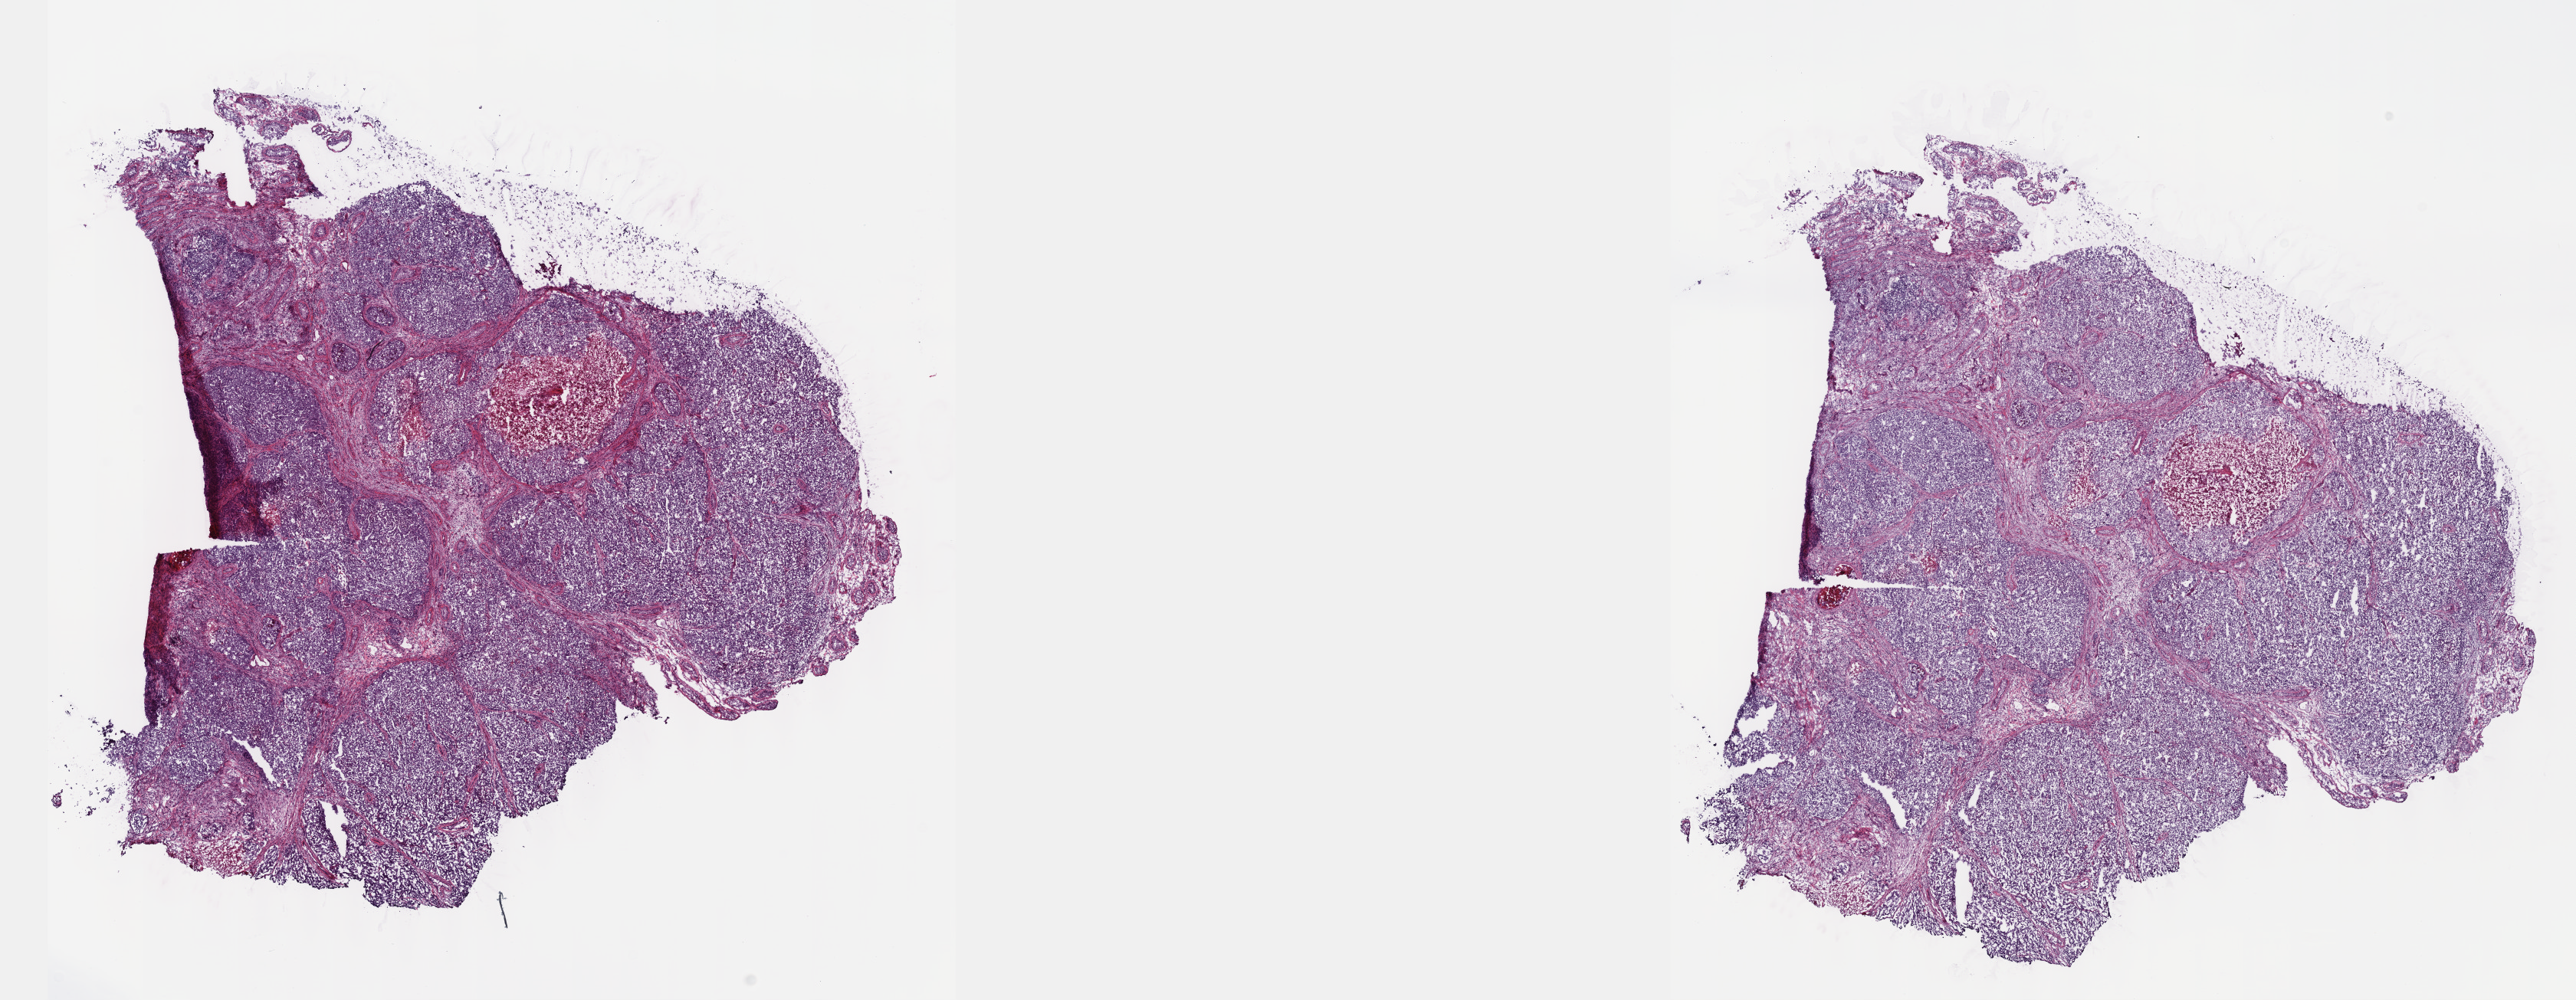
Digitized H&E-stained tissue section (whole slide) — whole scanned area (about 27.2 x 10.5 mm) shown as a low-resolution overview, frozen section, testis, primary tumour sample. Male patient; age at initial diagnosis 24 years. Composition of this section per pathologist review: tumour cells 100%, tumour nuclei 75%, normal cells 0%, stromal cells 0%, necrosis 0%. Inflammatory infiltration, as recorded: lymphocyte infiltration 2%, monocyte infiltration 0%, neutrophil infiltration 0%.
* pathologic diagnosis: Embryonal carcinoma, NOS
* laterality: right
* AJCC pathologic stage: IS